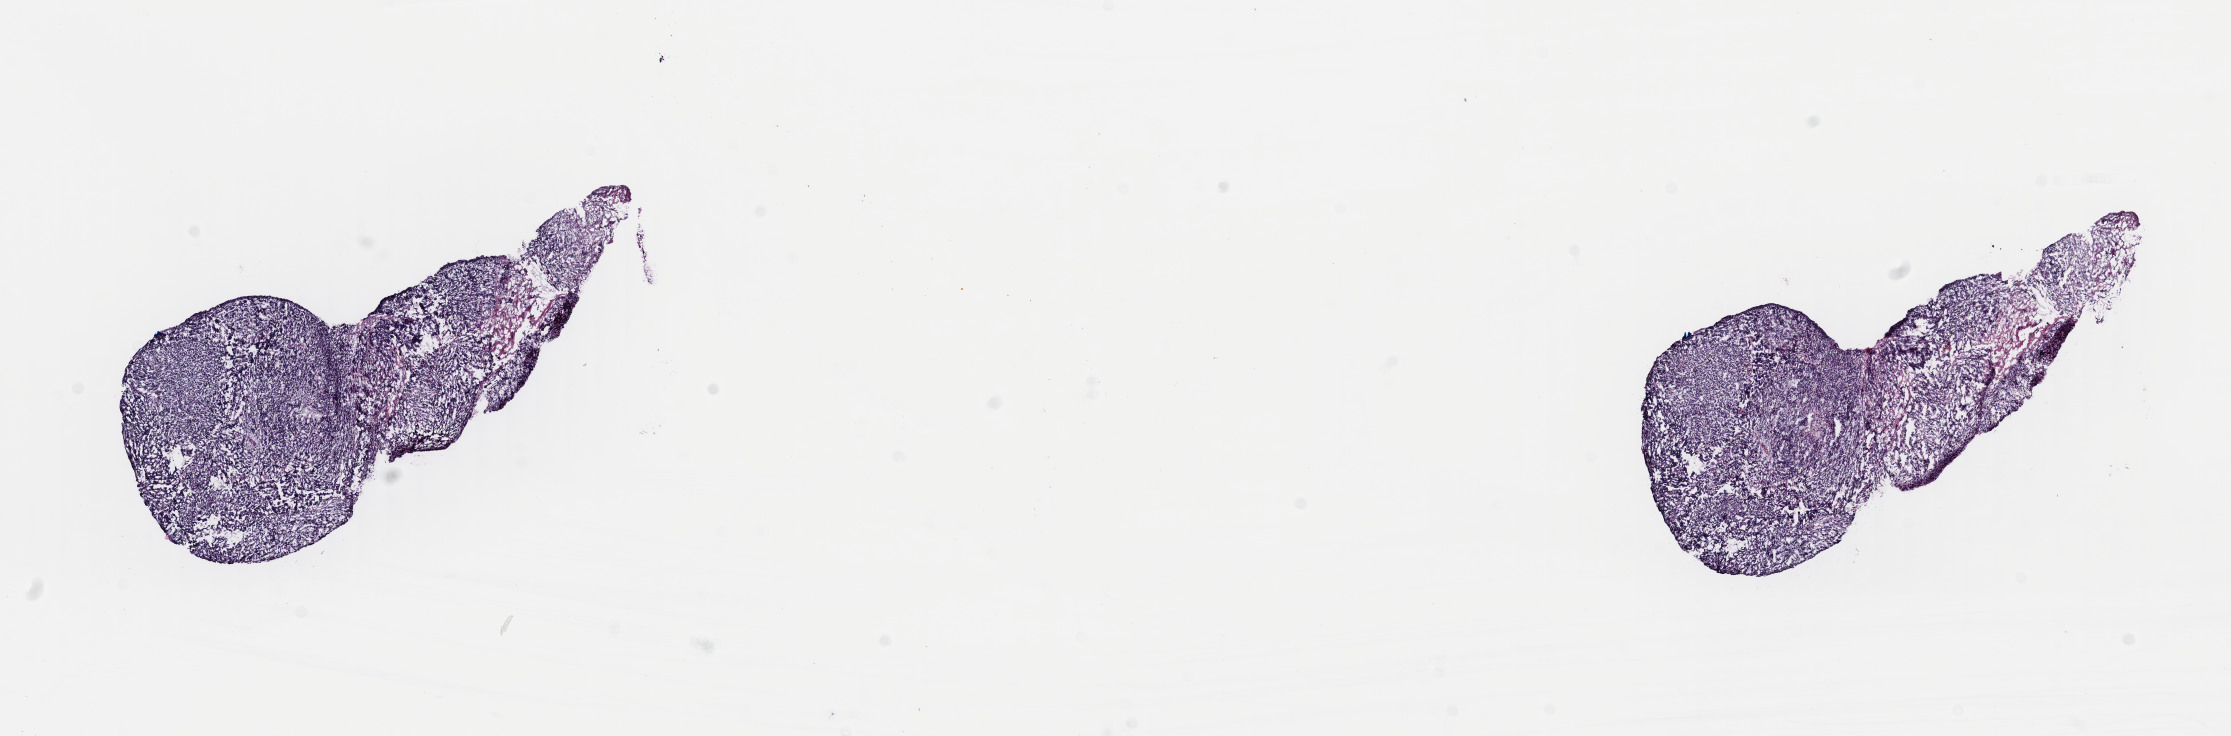
Hematoxylin and eosin (H&E) stained whole-slide image, a low-resolution overview of the entire scanned area, about 17.6 x 5.8 mm (slide scanned at 40x); frozen section from the top of the tissue portion; sample: primary tumour, uterus. Female, age 66 years at initial diagnosis. Pathologist review of this section (percent, as recorded): tumour cells 90%, tumour nuclei 90%, normal cells 0%, stromal cells 10%, necrosis 0%. Infiltration values recorded for this section: lymphocyte infiltration 60%, monocyte infiltration 10%, neutrophil infiltration 20%.
Pathologic diagnosis: Carcinosarcoma, NOS (isthmus uteri). FIGO stage: II.